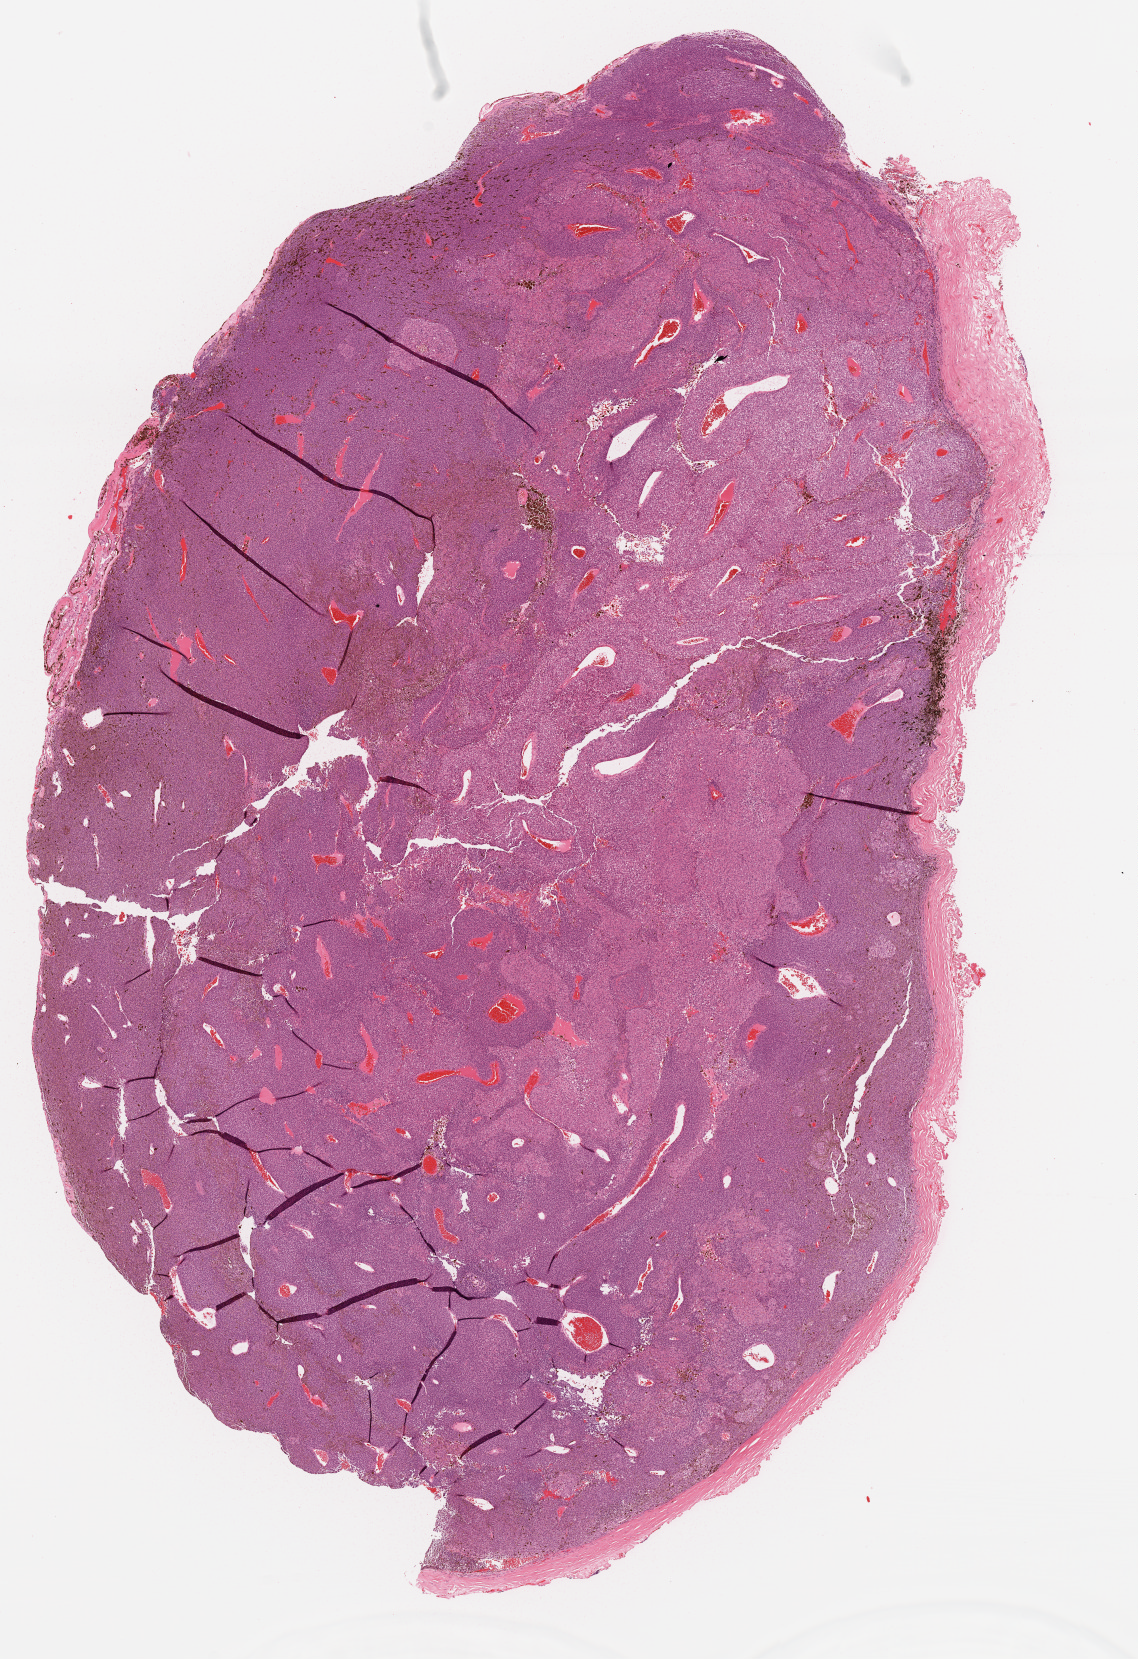
Digitized Hematoxylin and eosin (H&E) stained tissue section (whole slide) — a low-resolution overview of the entire scanned area, about 9.2 x 13.4 mm (slide scanned at 20x); formalin-fixed paraffin-embedded (FFPE) diagnostic section; uvea, primary tumour sample. Female, age 66 years at initial diagnosis. Composition of this section per pathologist review: tumour cells 100%, tumour nuclei 80%, normal cells 0%, stromal cells 0%, necrosis 0%. Inflammatory infiltration, as recorded: lymphocyte infiltration 1%, monocyte infiltration 0%, neutrophil infiltration 0%.
Histologic diagnosis: Pheochromocytoma, malignant (choroid). Laterality: right. AJCC pathologic stage: IIB.